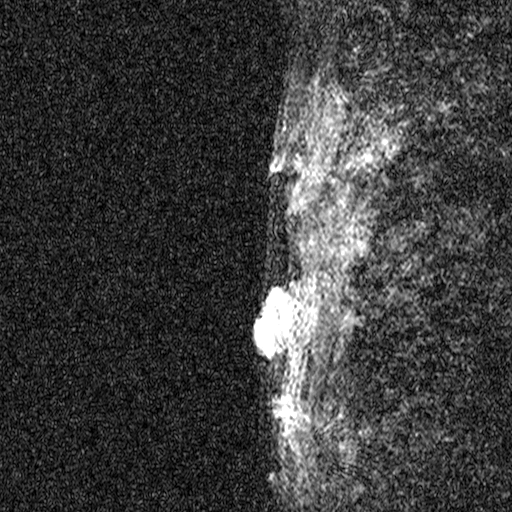
Breast MRI (dynamic contrast-enhanced), one sagittal slice; position 43 of 44 along the scan axis; dynamic contrast-enhanced study with each time point stored as its own series, time point 2 of 3 at this slice position (early post-contrast, ordered by acquisition time); 1.5 T; TE 4.5 ms, TR 11 ms; 2.05 mm slice thickness; 512 × 512 image matrix, field of view 200 × 200 mm. Female patient, age 44 years. Case-level facts recorded for this patient, not image findings: setting: breast cancer imaged before/during neoadjuvant chemotherapy; receptor status: HR-positive, HER2-negative.
Outlined on this slice (semi-automatically segmented with operator editing):
- analysis volume of interest (the breast-tissue region the enhancement analysis was run in; not a lesion): bounding box (x1, y1, x2, y2) in pixels: (204, 254, 317, 401)
- tumour enhancement mask (voxels above the 90 % enhancement threshold inside the analysis volume of interest): (254, 283, 293, 386)